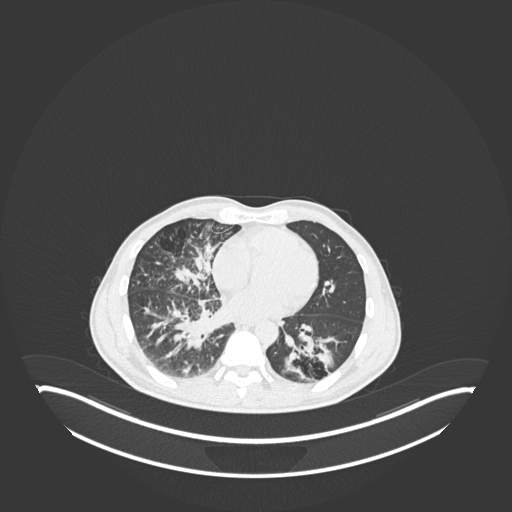
Chest CT, one axial slice. Slice 97 of 237 in the series (ordered by position). 120 kVp. Lung window (W 1500 / L -600 HU). 1 mm slice thickness. 512 × 512 image matrix, field of view 500 × 500 mm. Male patient, age 49 years. From the clinical record (not read from this slice): clinical TNM (as recorded): T2b N1 M0.
Annotated regions visible in this slice (bounding box drawn by a radiologist):
- lung tumour (recorded histology: adenocarcinoma): box from (x=283, y=330) to (x=340, y=382) px